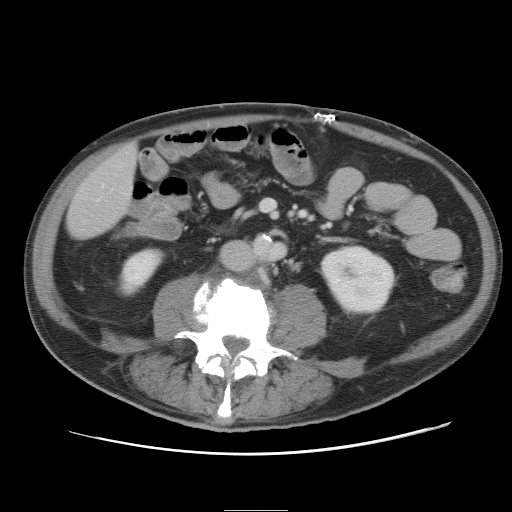
Contrast-enhanced abdominal CT, one axial slice. Slice 5 of 89 in the series (ordered by position). Intravenous contrast given. Soft-tissue window (W 400 / L 40 HU). 5 mm slice thickness. 512 × 512 image matrix. Male patient, age 69 years. Case-level facts recorded for this patient, not image findings: diagnosis: colorectal cancer liver metastases, imaged before liver resection; multiple liver metastases: no; largest metastasis: 8.5 cm; disease in both lobes: no.
Annotated regions visible in this slice (manually delineated by an expert):
- liver: bounding box (x1, y1, x2, y2) in pixels: (68, 145, 137, 239)
- planned liver remnant (the part of the liver to remain after resection): (68, 144, 138, 238)